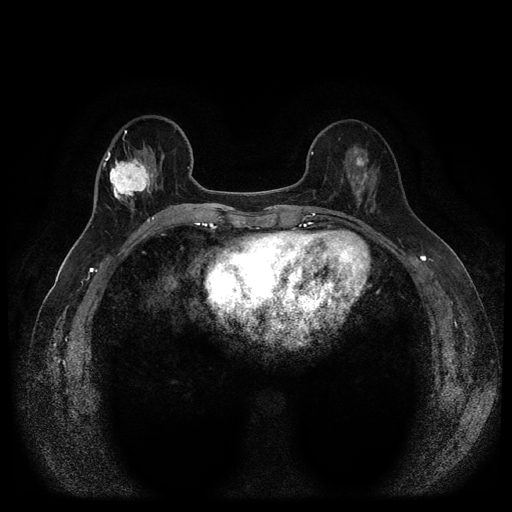
Breast MRI (dynamic contrast-enhanced, multi-phase), one axial slice; position 37 of 116 along the scan axis; dynamic contrast-enhanced series, time point 2 of 5 at this slice position (early post-contrast); 1.5 T; TE 2.6 ms, TR 5.4 ms; 512 × 512 image matrix. Patient: female, 56 years.
Structures marked on this image (semi-automatic segmentation, software-assisted and operator-edited):
- breast lesion (labelled benign in the annotation): bounding box (x1, y1, x2, y2) in pixels: (346, 145, 370, 208)
- breast lesion (labelled 'tumour' in the annotation; benign lesions carry a separate 'benign' label): (106, 146, 154, 205)